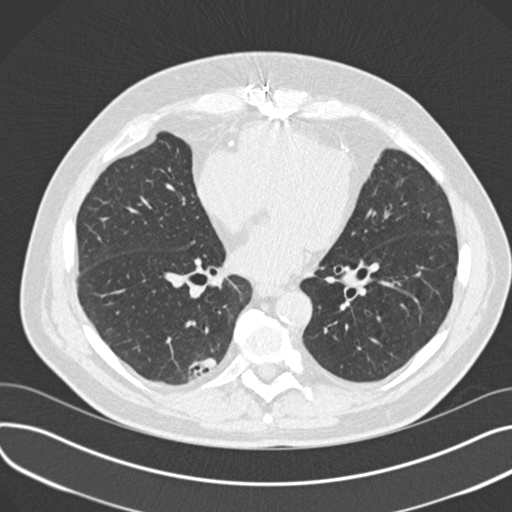
Low-dose screening chest CT, one axial slice; slice 77 of 177 in the series (ordered by position); lung window (W 1500 / L -600 HU); 2 mm slice thickness; 512 × 512 image matrix.
Outlined on this slice (manually delineated by an expert):
- lesion 1 (tumor, lower lobe of right lung): box from (x=188, y=349) to (x=217, y=380) px